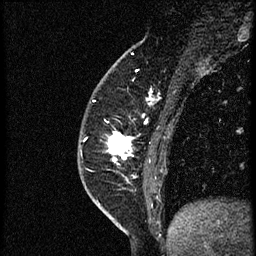
Breast MRI (dynamic contrast-enhanced), one sagittal slice. Position 19 of 56 along the scan axis. Dynamic contrast-enhanced study with each time point stored as its own series, time point 2 of 4 at this slice position (early post-contrast, ordered by acquisition time). 1.5 T. TE 4.2 ms, TR 18.9 ms. 2 mm slice thickness. 256 × 256 image matrix, field of view 200 × 200 mm. Female patient. Case-level facts recorded for this patient, not image findings: setting: breast cancer imaged before/during neoadjuvant chemotherapy; receptor status: HER2-positive.
Outlined on this slice (semi-automatic segmentation, software-assisted and operator-edited):
- analysis volume of interest (the breast-tissue region the enhancement analysis was run in; not a lesion): bounding box (x1, y1, x2, y2) in pixels: (110, 90, 174, 189)
- tumour enhancement mask (voxels above the 100 % enhancement threshold inside the analysis volume of interest): (110, 132, 135, 164)